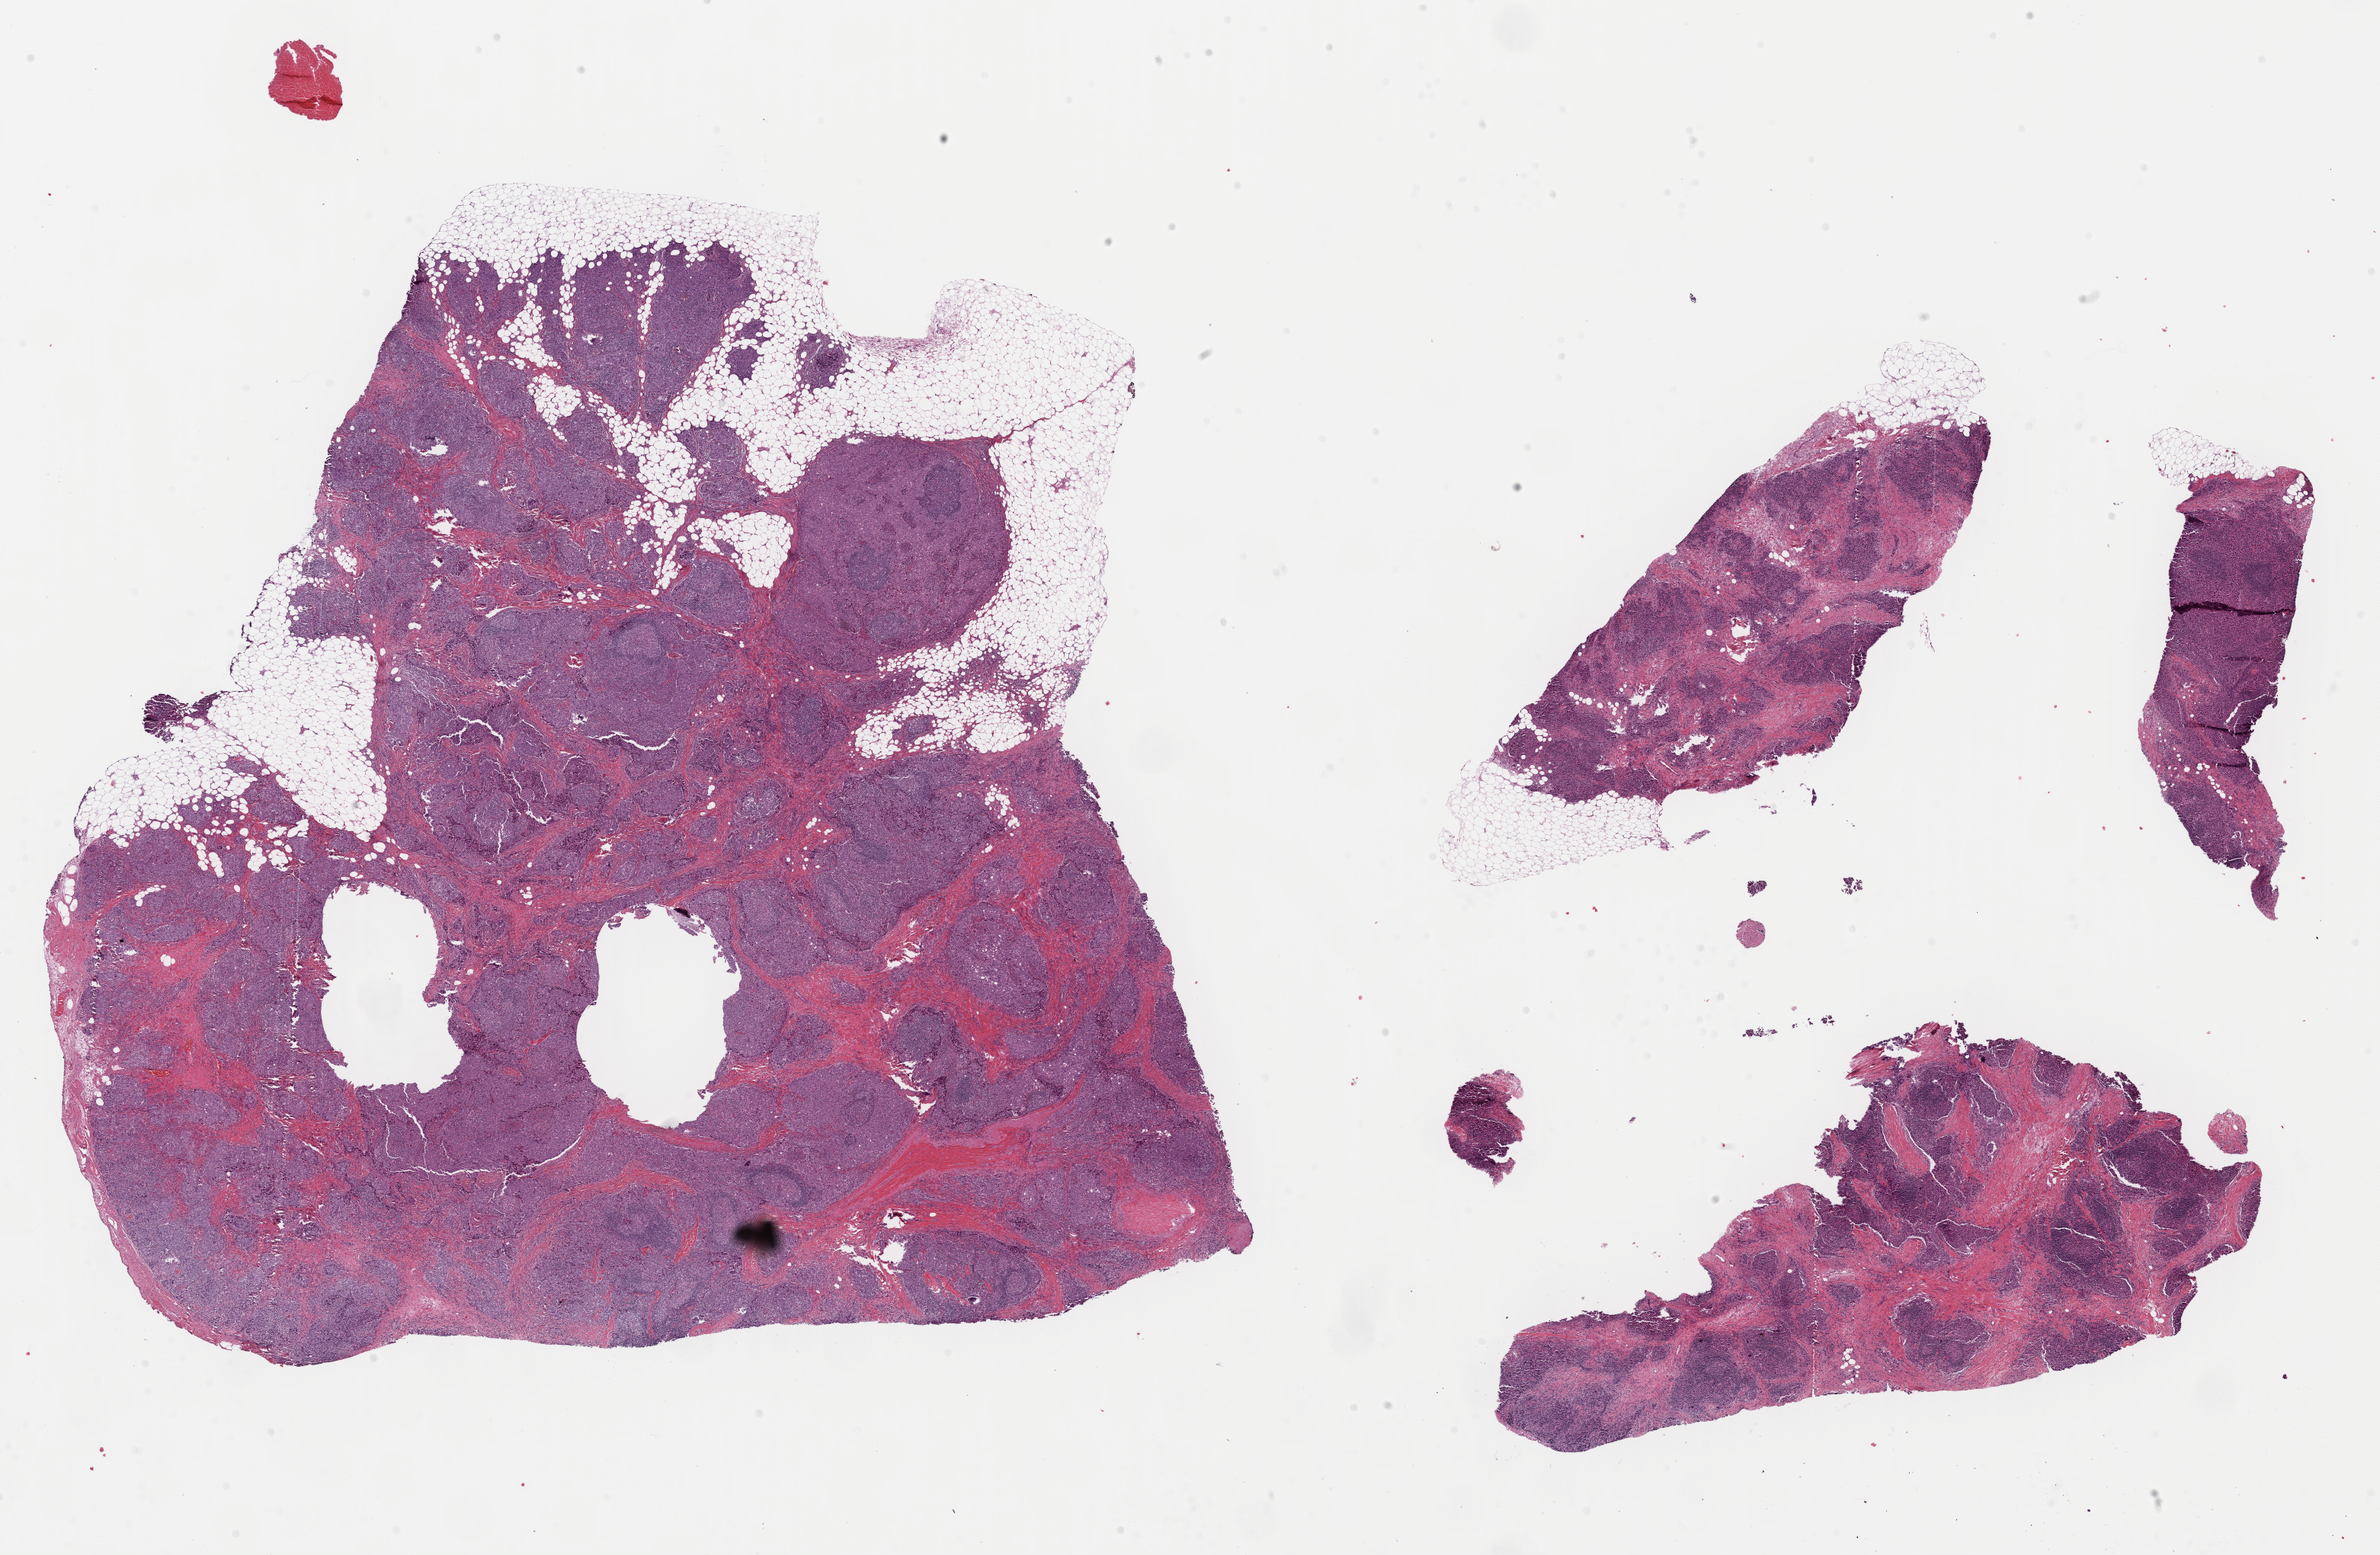
Whole-slide histology image, Hematoxylin and eosin (H&E) stained, low-resolution overview of the scanned area, about 24.7 x 16.1 mm (acquisition: 40x scan), formalin-fixed paraffin-embedded (FFPE) diagnostic section, breast, primary tumour sample. Female, age 65 years at initial diagnosis.
- histologic diagnosis: Infiltrating duct carcinoma, NOS
- lymph nodes positive (case pathology): 0 of 1 examined
- AJCC pathologic stage: IIA (6th edition)